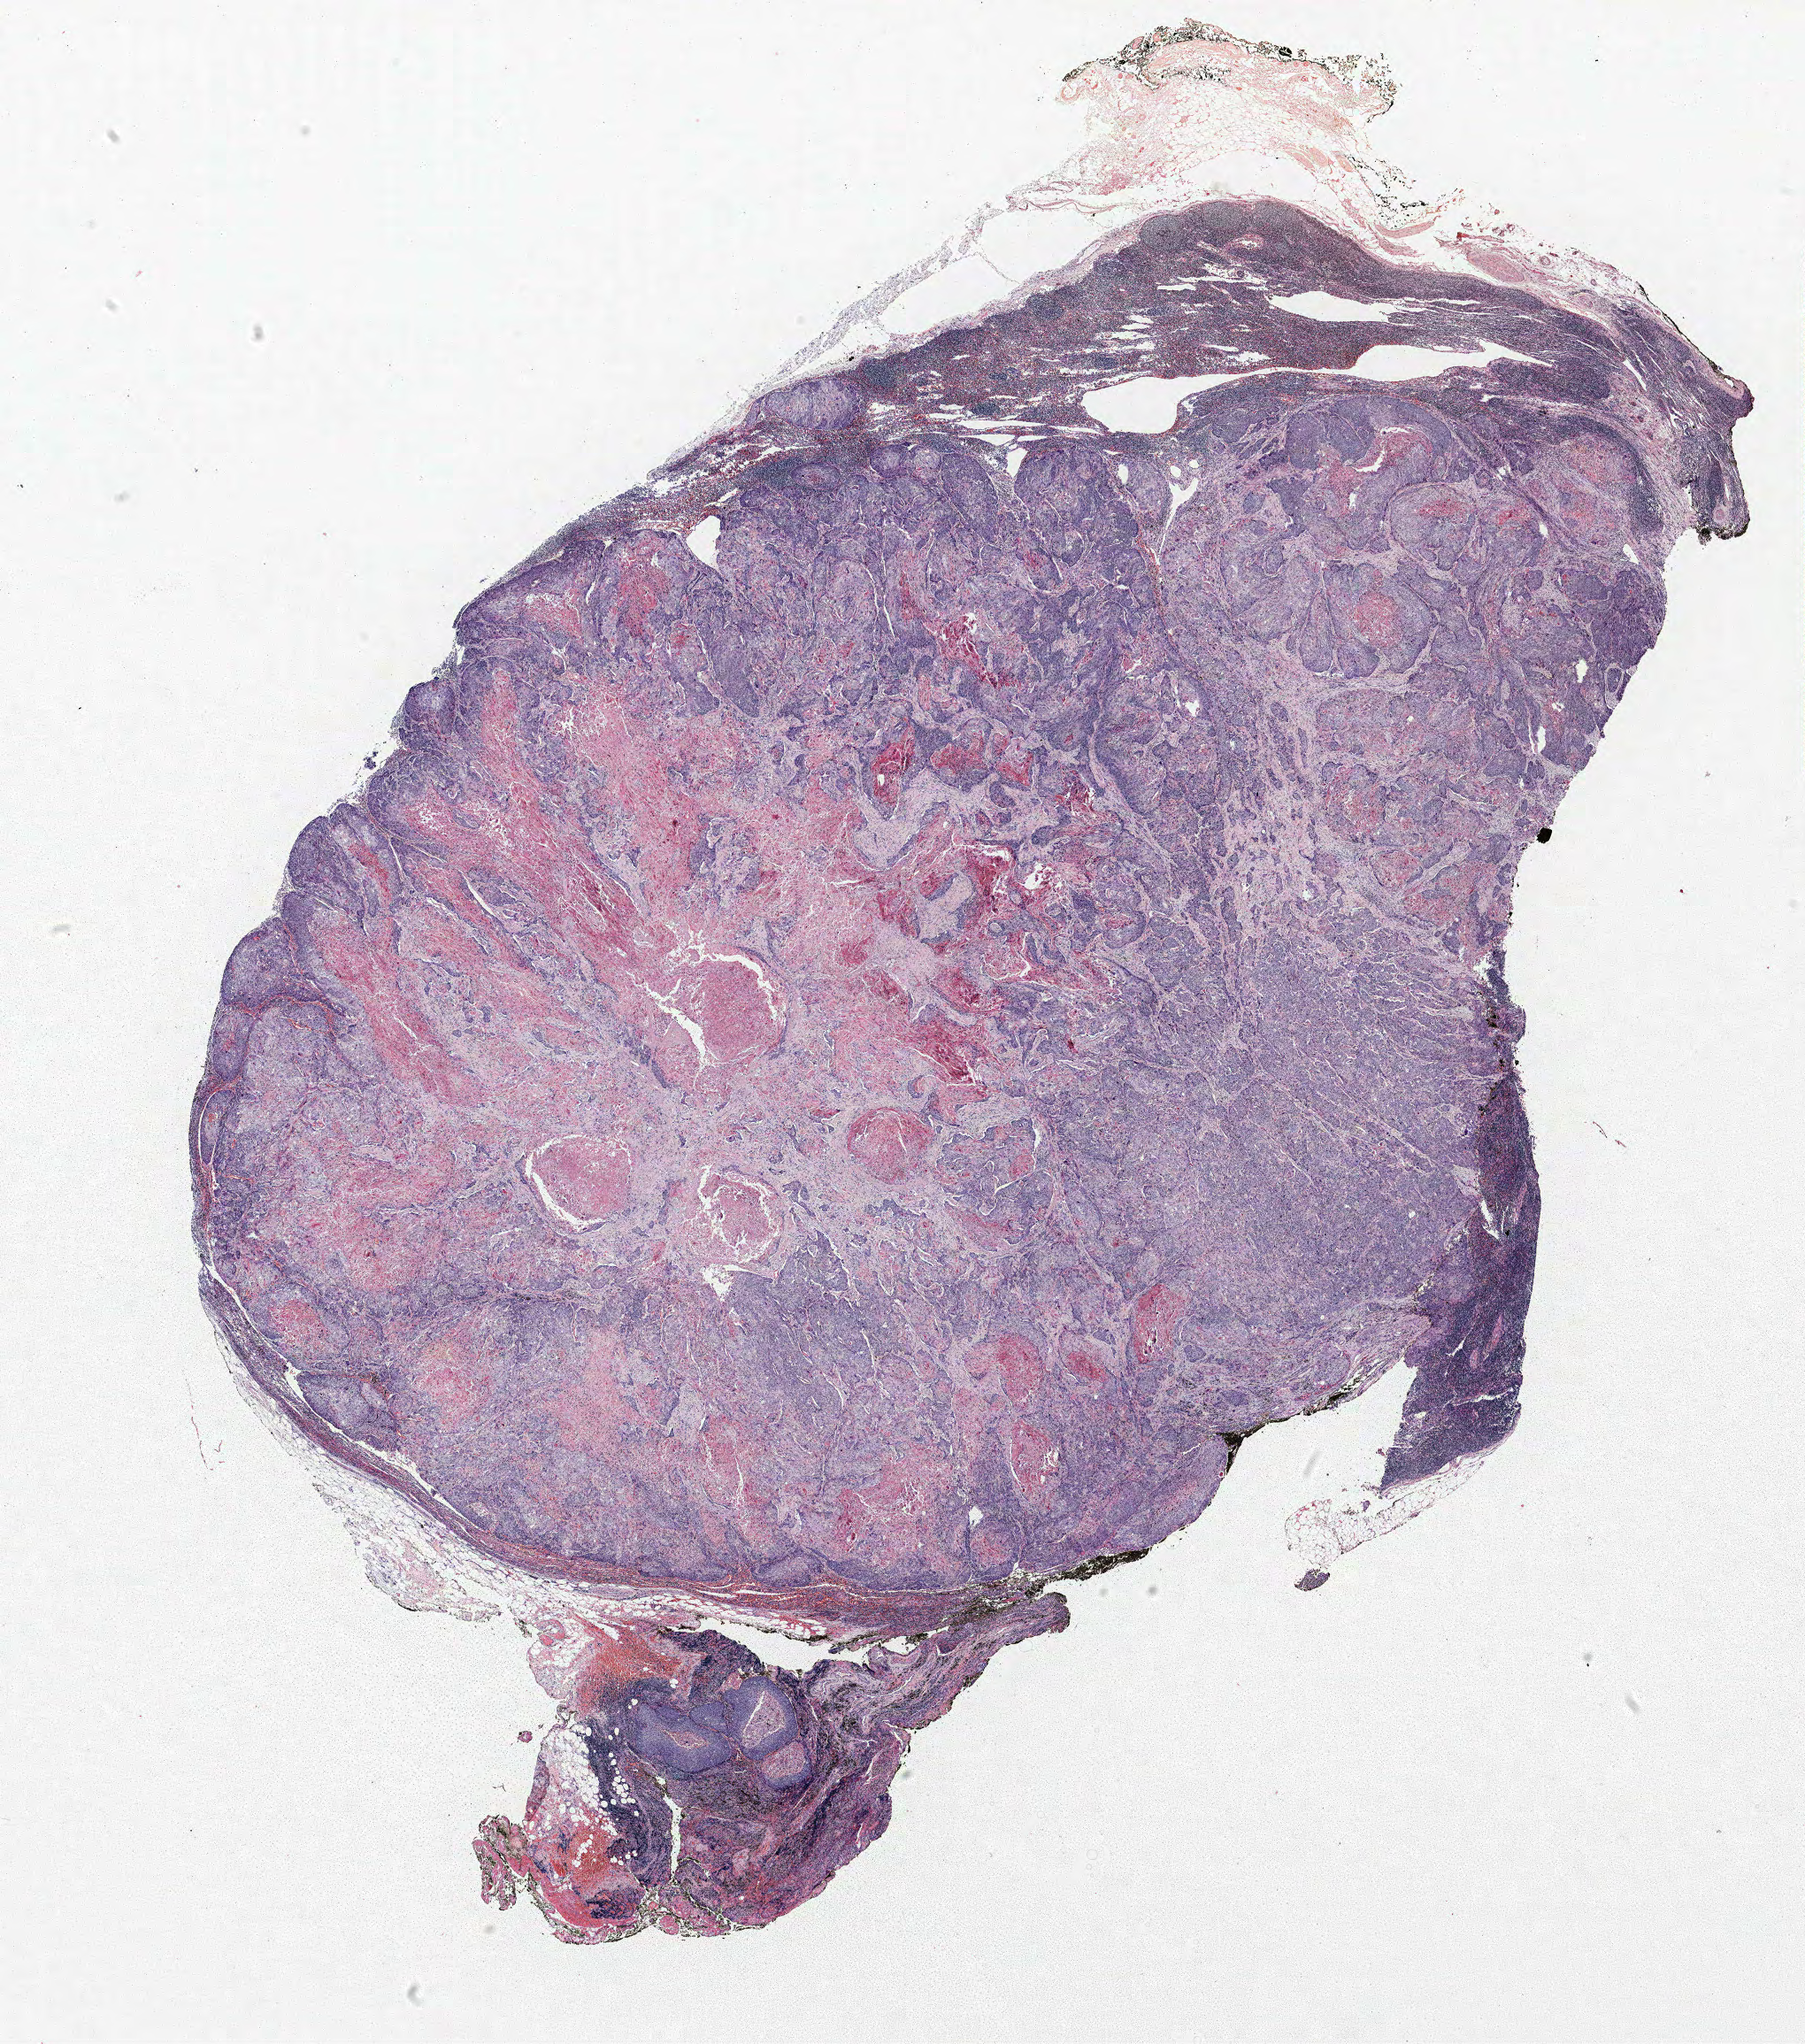
H&E whole-slide image — shown as a low-resolution overview of the whole scanned area (about 16.3 x 18.5 mm). FFPE section. Lung. Female patient, aged 63 at enrolment. Former smoker at enrolment. Grade: moderately differentiated (G2).
Tumour size (pathology): 42 mm. Primary tumour location (clinical record): right upper lobe. Stage (AJCC 6th edition): IIA. Participant's lung-cancer diagnosis: Squamous cell carcinoma, keratinizing, NOS (ICD-O-3 8071/3). ICD-O-3 topography: upper lobe of lung (C34.1).